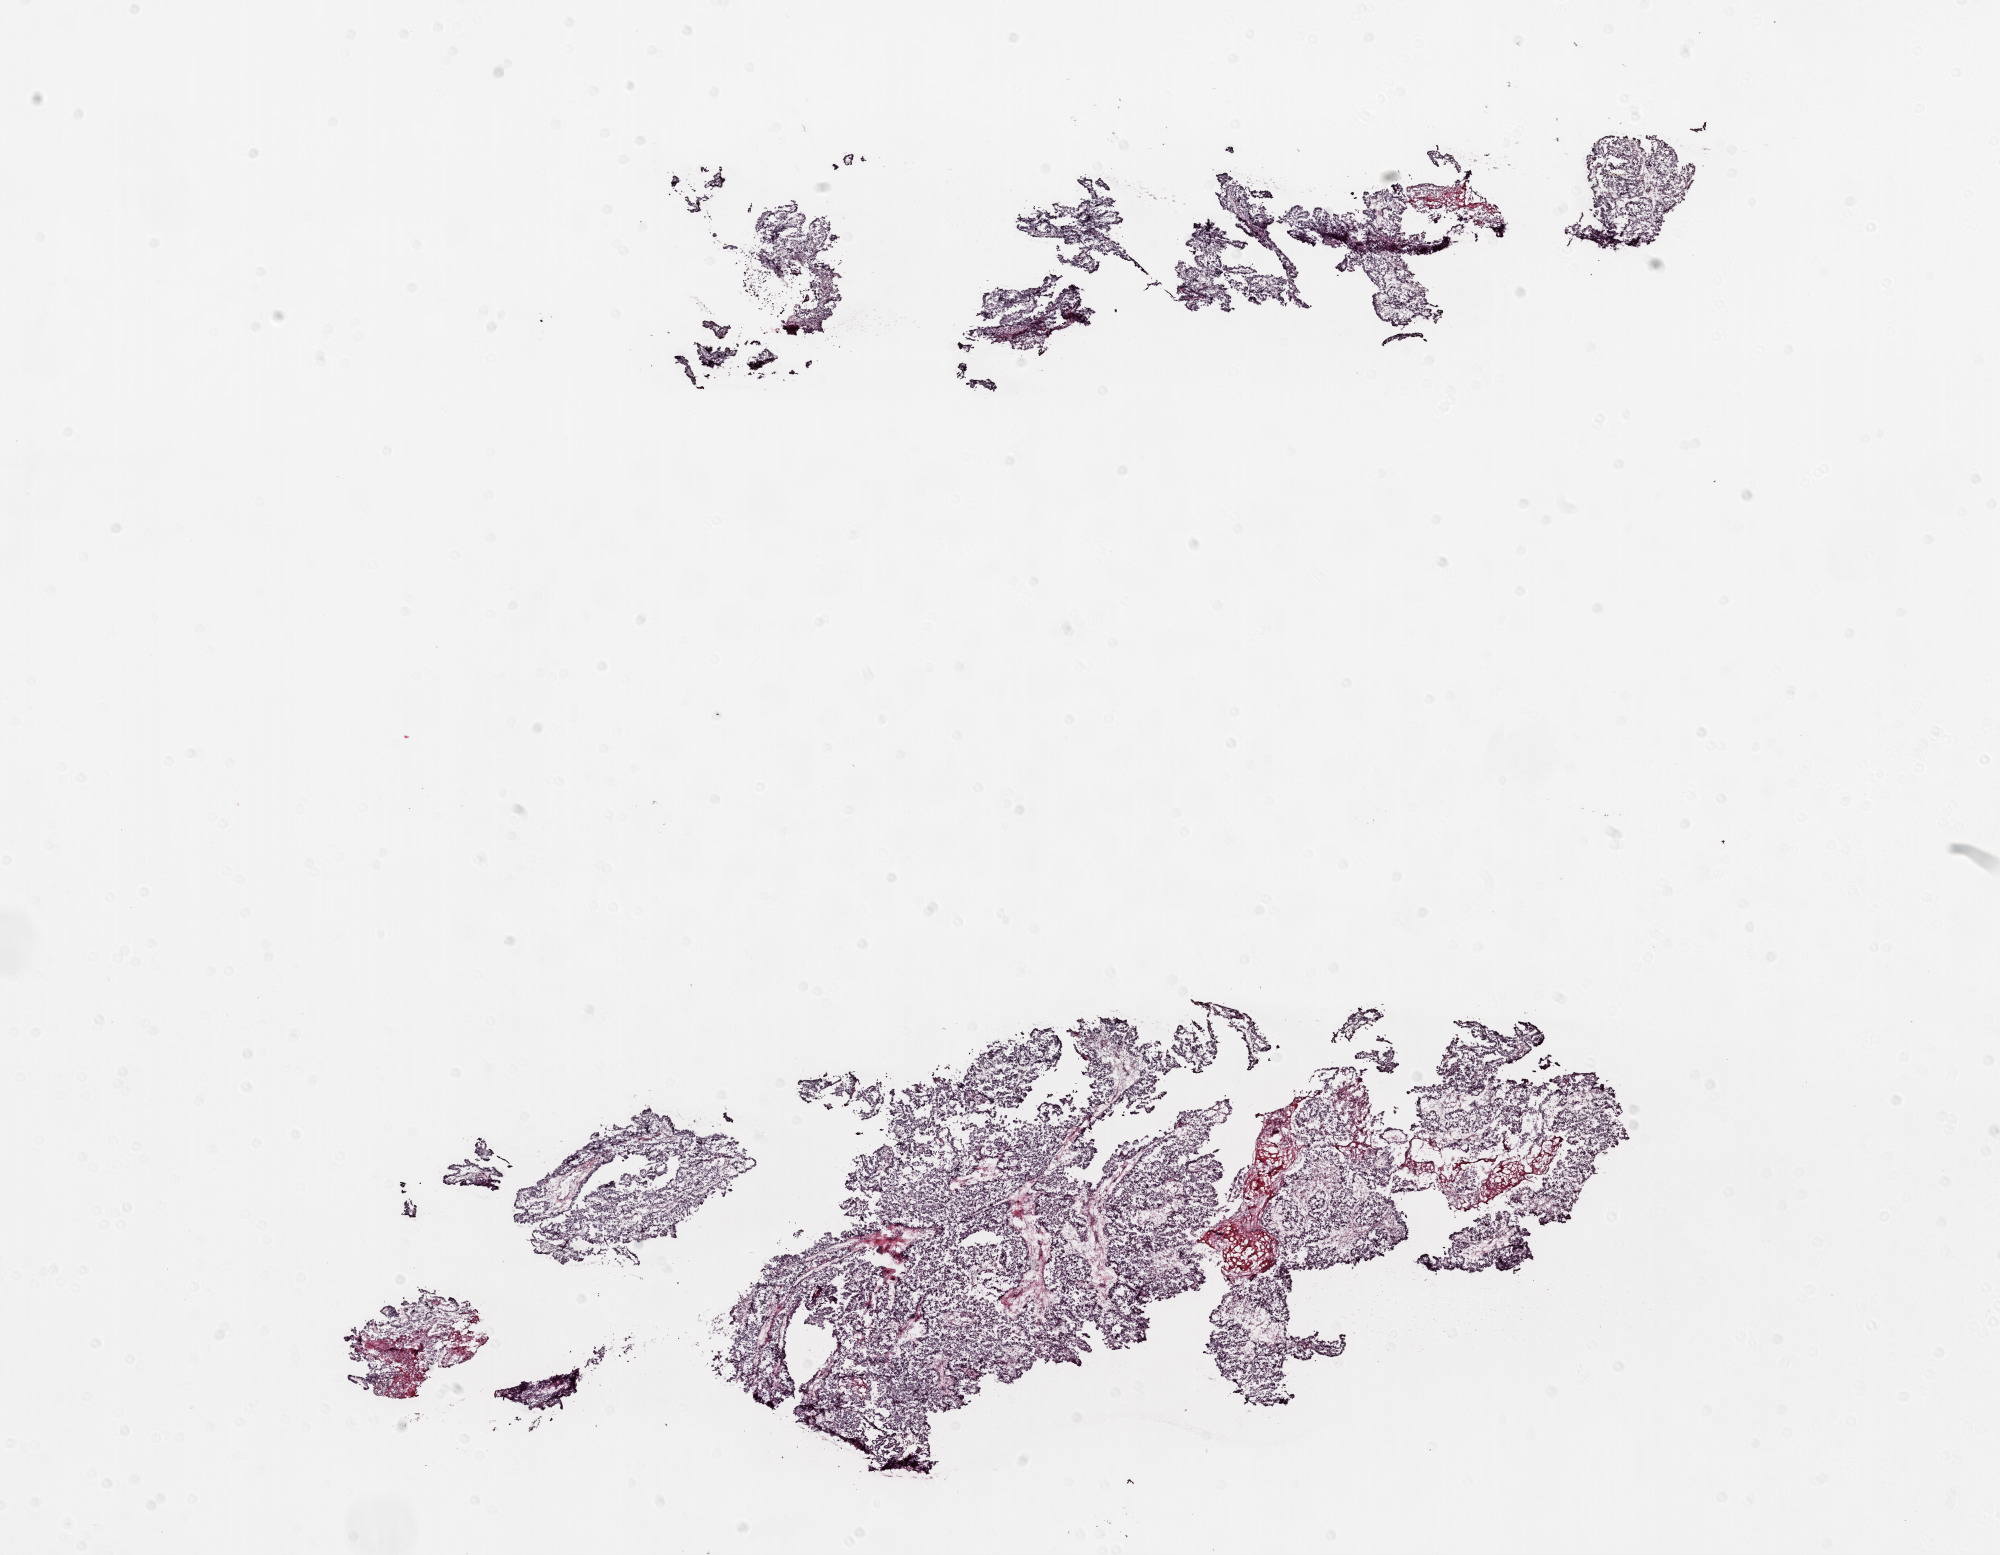
Digitized H&E tissue section (whole slide), whole scanned area (about 16.0 x 12.5 mm, slide scanned at 20x) shown as a low-resolution overview; frozen section; primary tumour sample from the ovary. Patient: female, age at initial diagnosis 56 years. Histologic grade: G3 (poorly differentiated). Composition of this section per pathologist review: tumour cells 80%, tumour nuclei 90%, normal cells 0%, stromal cells 20%, necrosis 0%.
Pathologic diagnosis: Serous cystadenocarcinoma, NOS. Laterality: bilateral.